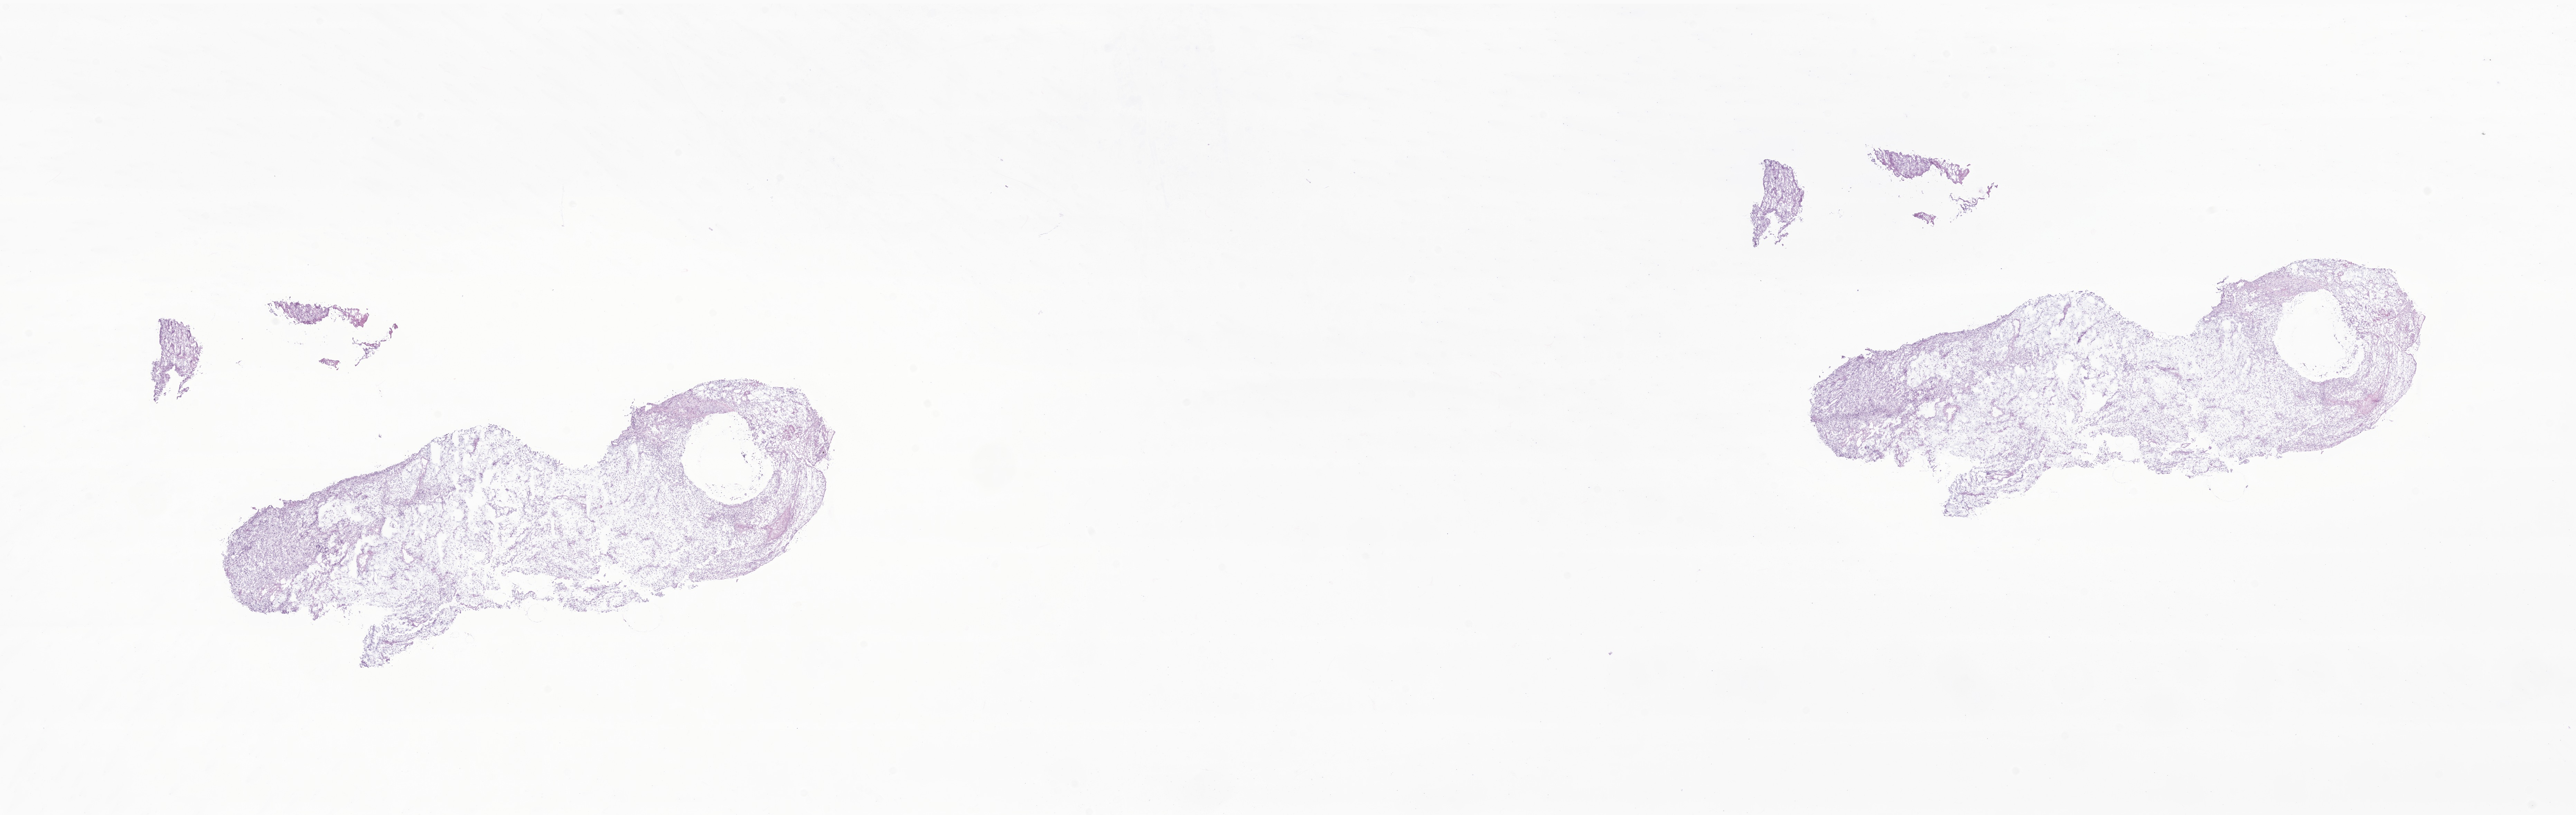
Digitized H&E-stained section of tumor tissue from the nasopharynx — low-resolution overview of the scanned area, about 31.4 x 9.9 mm. Frozen section (OCT-embedded). Patient male; age 106 months (8 years 10 months).
Diagnosis: Embryonal rhabdomyosarcoma, NOS.